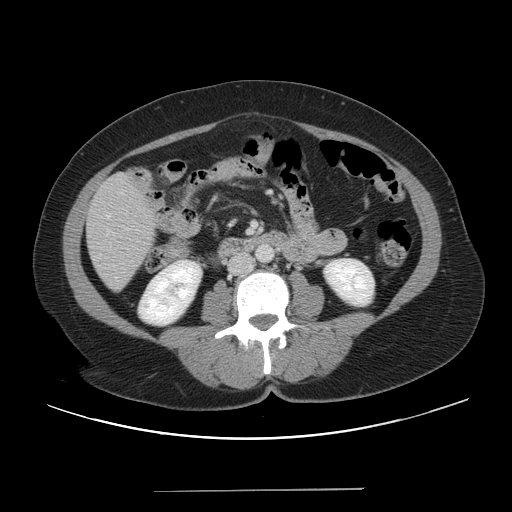
Contrast-enhanced abdominal CT, one axial slice; slice 10 of 56 in the series (ordered by position); 120 kVp; intravenous contrast given; soft-tissue window (W 400 / L 40 HU); 5 mm slice thickness; 512 × 512 image matrix. Female patient, age 54 years. Case-level facts recorded for this patient, not image findings: diagnosis: colorectal cancer liver metastases, imaged before liver resection; multiple liver metastases: yes; largest metastasis: 3.2 cm; disease in both lobes: yes.
Outlined on this slice (expert manual segmentation):
- liver: bounding box [x1, y1, x2, y2] px = [87, 173, 156, 292]